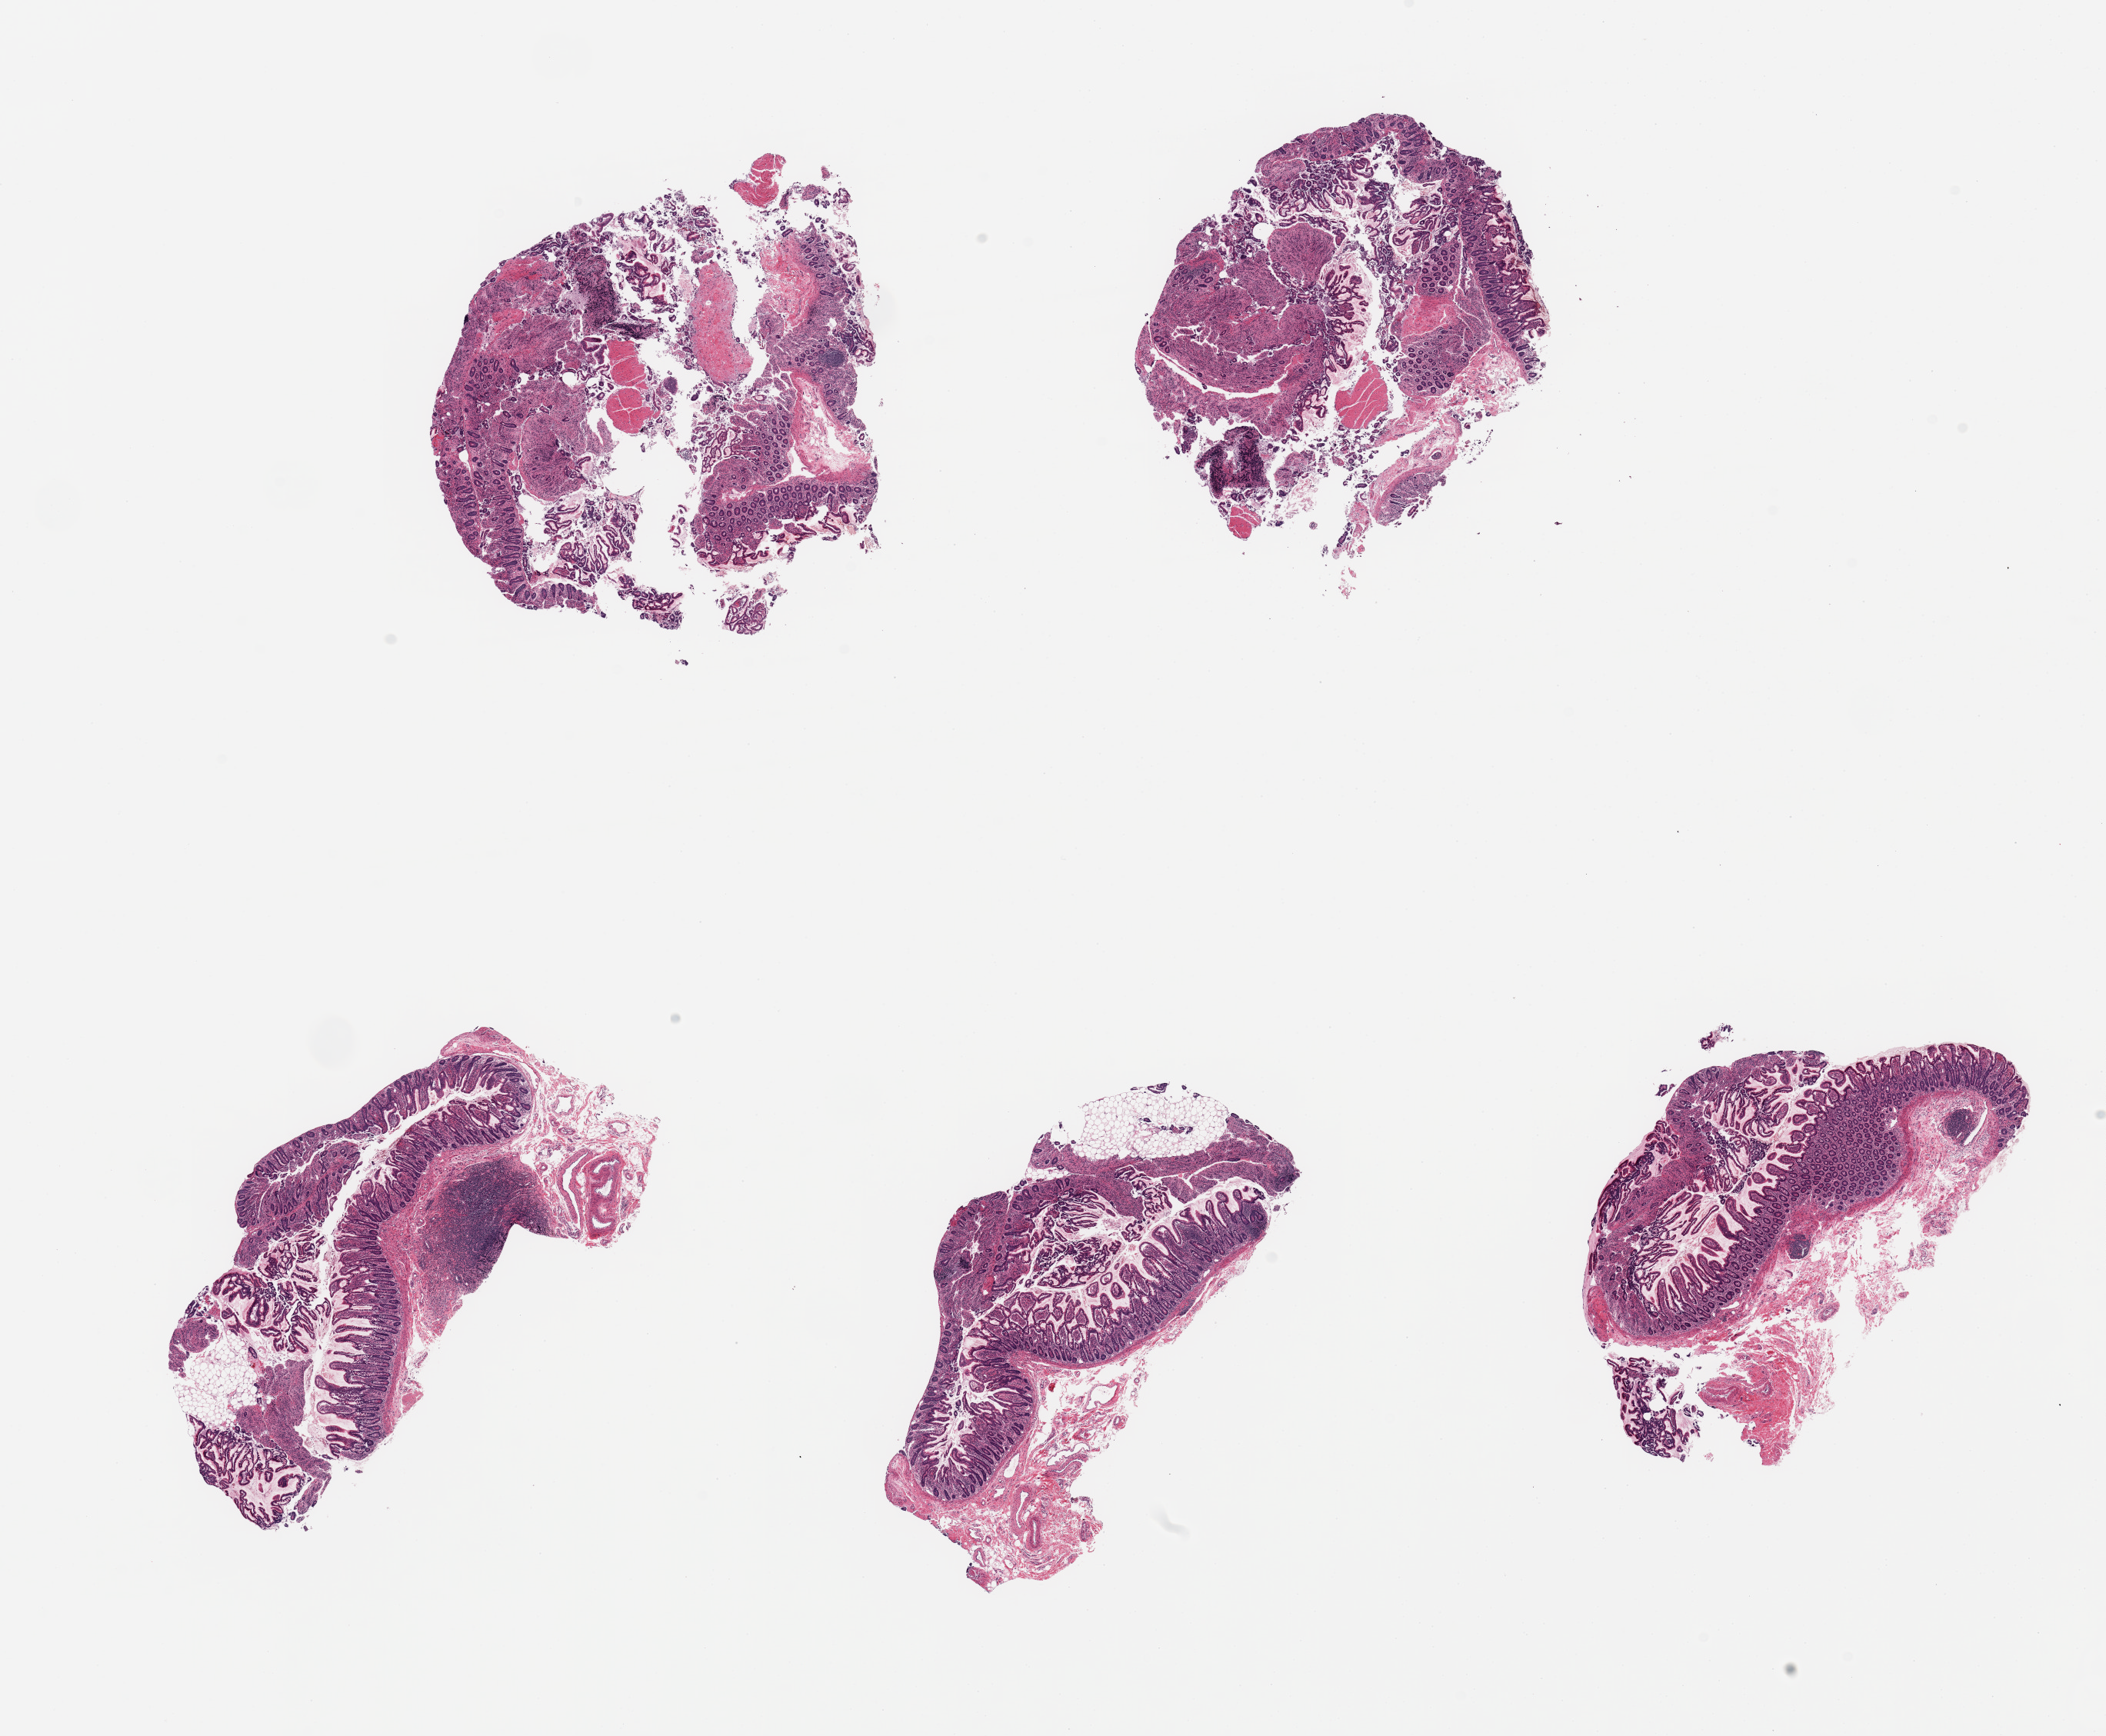
Digitized H&E-stained section, shown as a low-resolution overview of the whole scanned area (about 21.7 x 17.9 mm). PAXgene-fixed, paraffin-embedded tissue. Target tissue: ileum. Tissue donor sample. Donor: female.
- reviewer comment on this tissue sample: 5 pieces; several lymphoid nodules in 3 pieces; well dissected